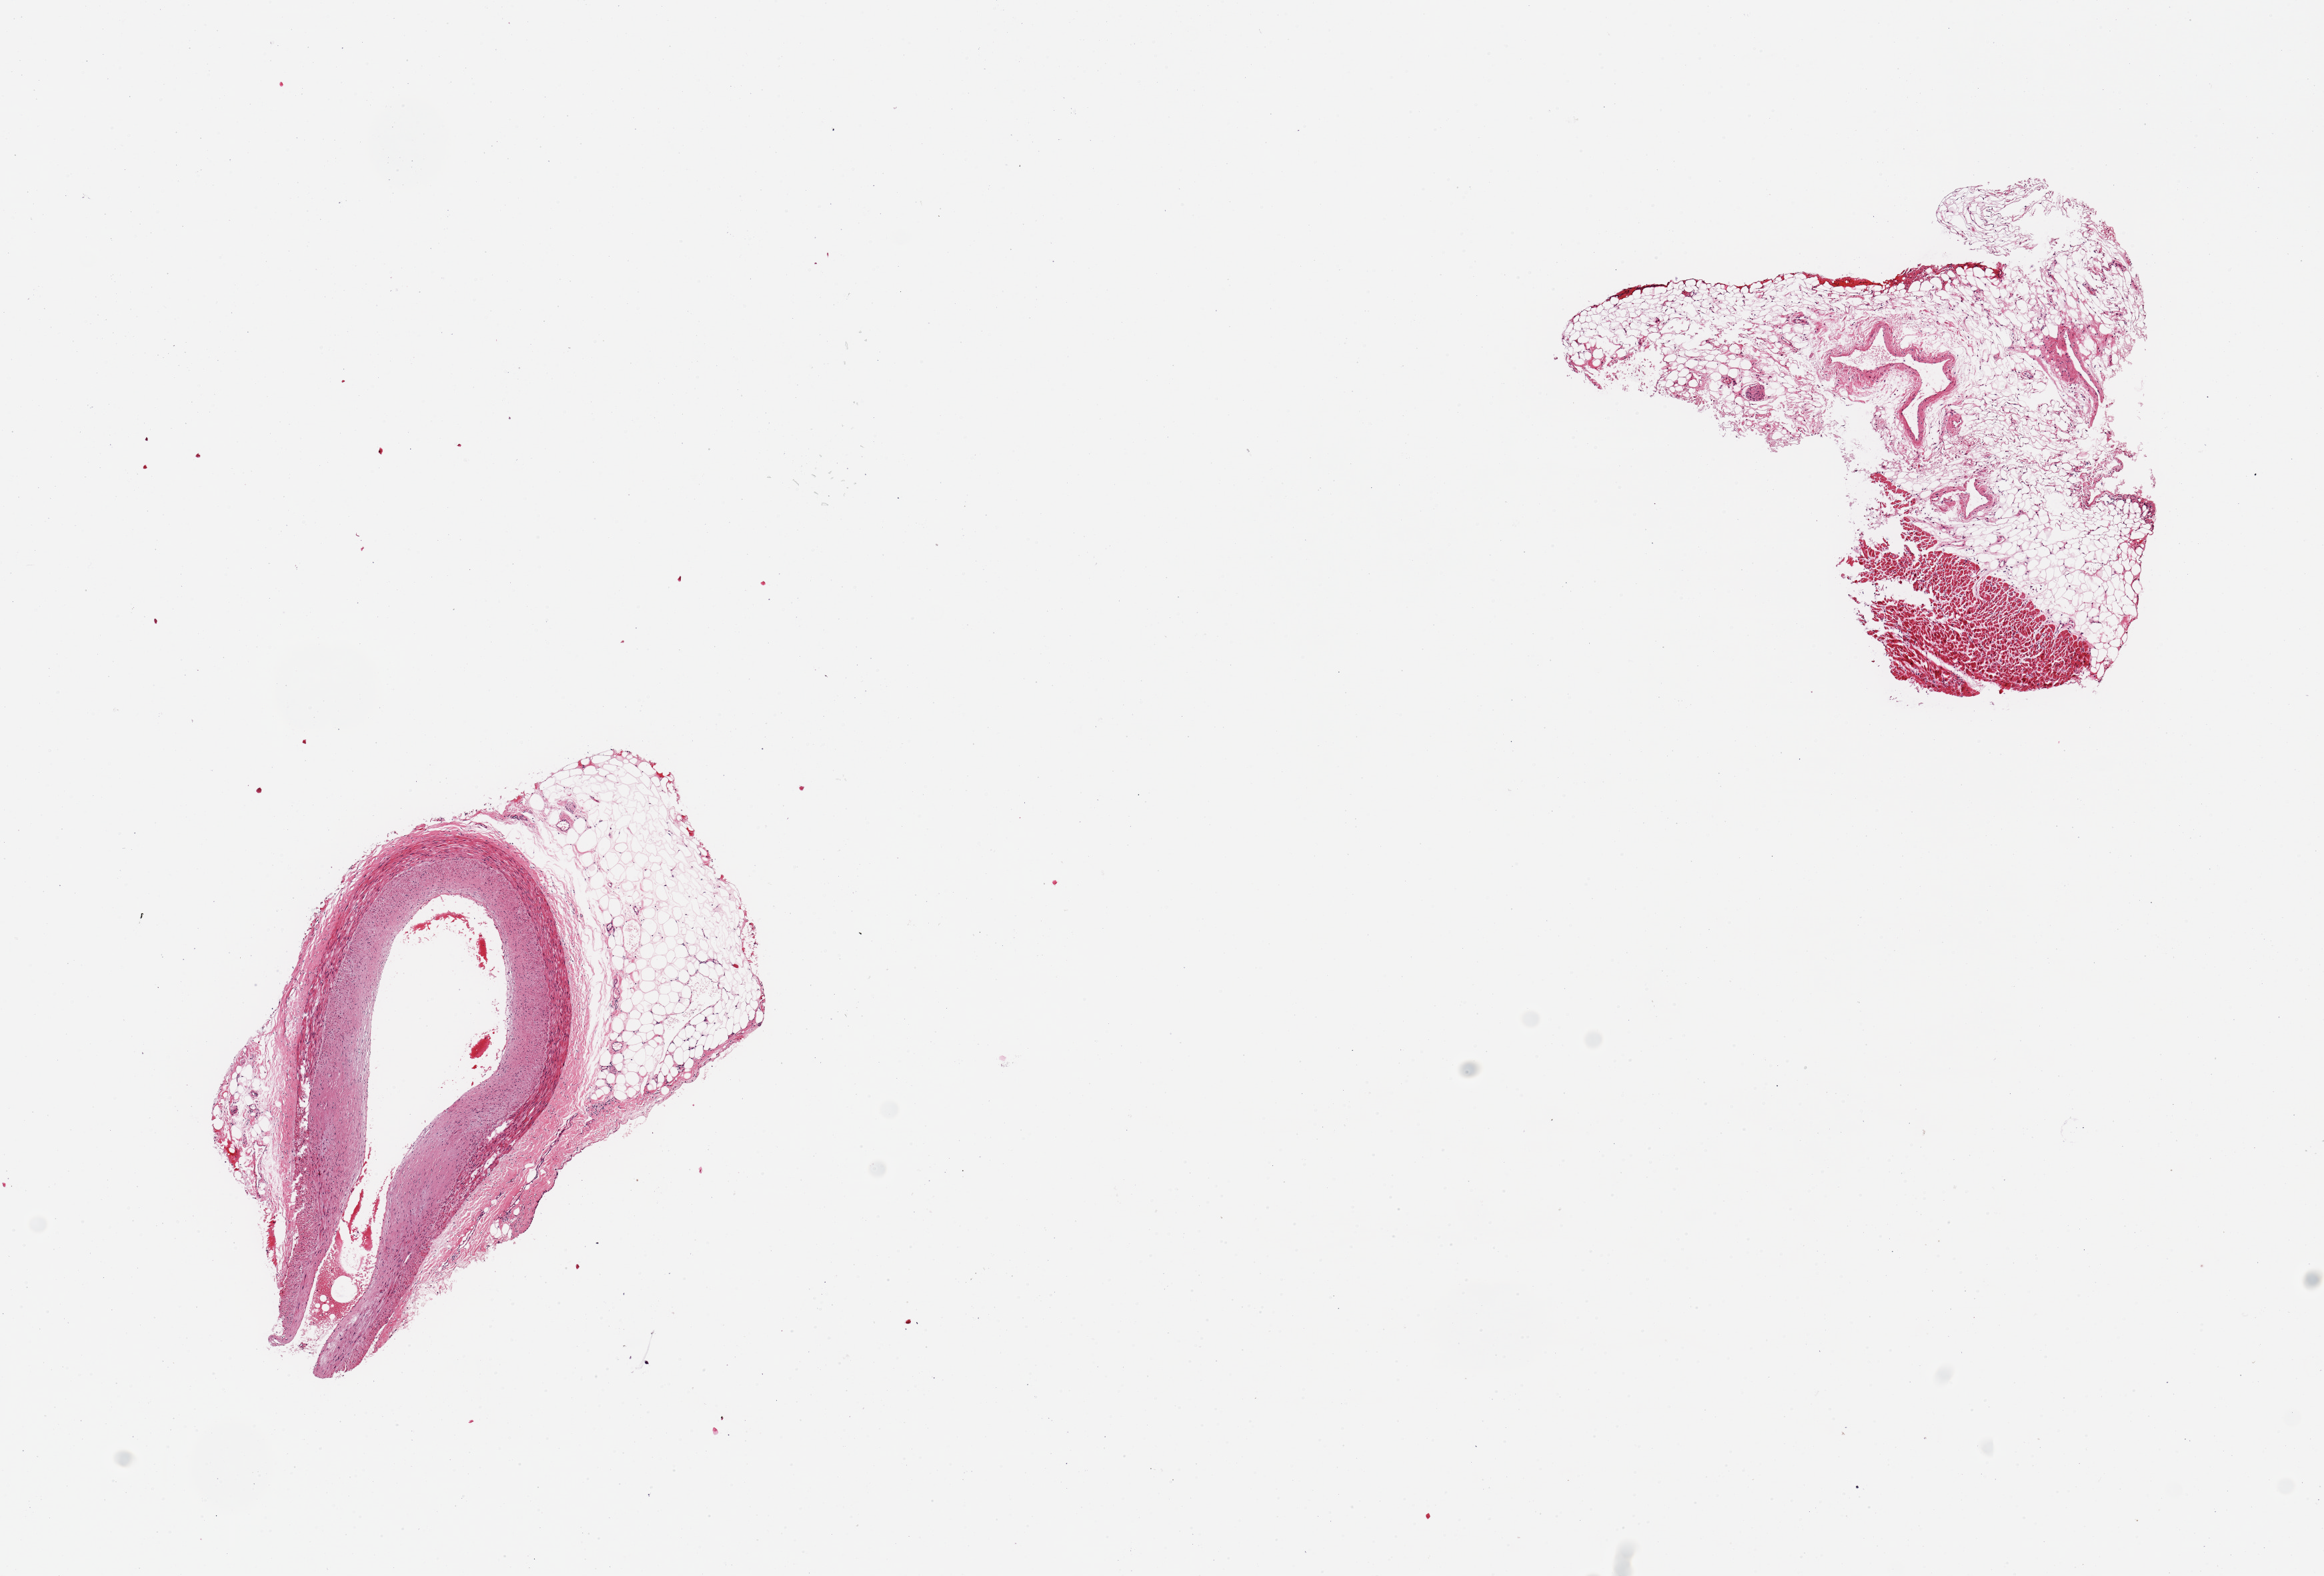
Whole-slide image, H&E stain, brightfield — whole scanned area (about 13.8 x 9.3 mm, acquisition: 20x scan) shown as a low-resolution overview. PAXgene-fixed paraffin-embedded (PFPE) section. Sampled site (target tissue): coronary artery. Tissue donor sample. Donor: female.
* pathologist's review note for this sample: 1 piece artery, no atherosis, adherent fat up to ~1mm; other piece is epicardial fat/myocardium